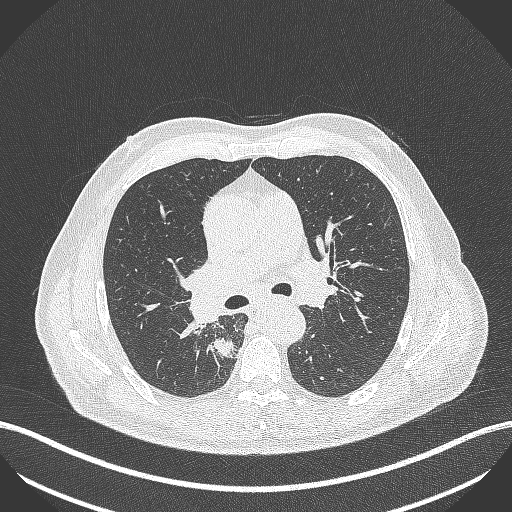
Chest CT, one axial slice. Position 283 of 451 along the scan axis. 100 kVp. Lung window (W 1500 / L -600 HU). 1 mm slice thickness. 512 × 512 image matrix, field of view 400 × 400 mm. Male patient, age 61 years. From the clinical record (not read from this slice): clinical TNM (as recorded): T1 N0 M0; histopathological grade: G3.
Annotated regions visible in this slice (bounding box drawn by a radiologist):
- lung tumour (recorded histology: small cell carcinoma): bounding box [x1, y1, x2, y2] px = [212, 336, 237, 362]